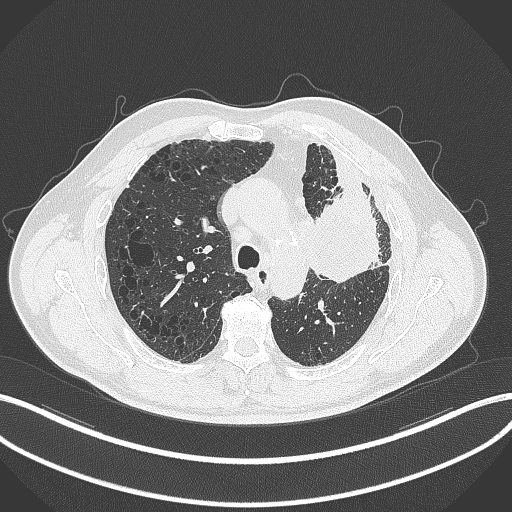
Chest CT, one axial slice. Position 218 of 297 along the scan axis. 120 kVp. Lung window (W 1500 / L -600 HU). 1 mm slice thickness. 512 × 512 image matrix. Patient: male, 68 years. From the clinical record (not read from this slice): clinical TNM (as recorded): T3 N3 M1.
Annotated regions visible in this slice (rectangle marked by the reading radiologist):
- lung tumour (recorded histology: adenocarcinoma): bounding box <315,187,382,291> (left, top, right, bottom; pixels)